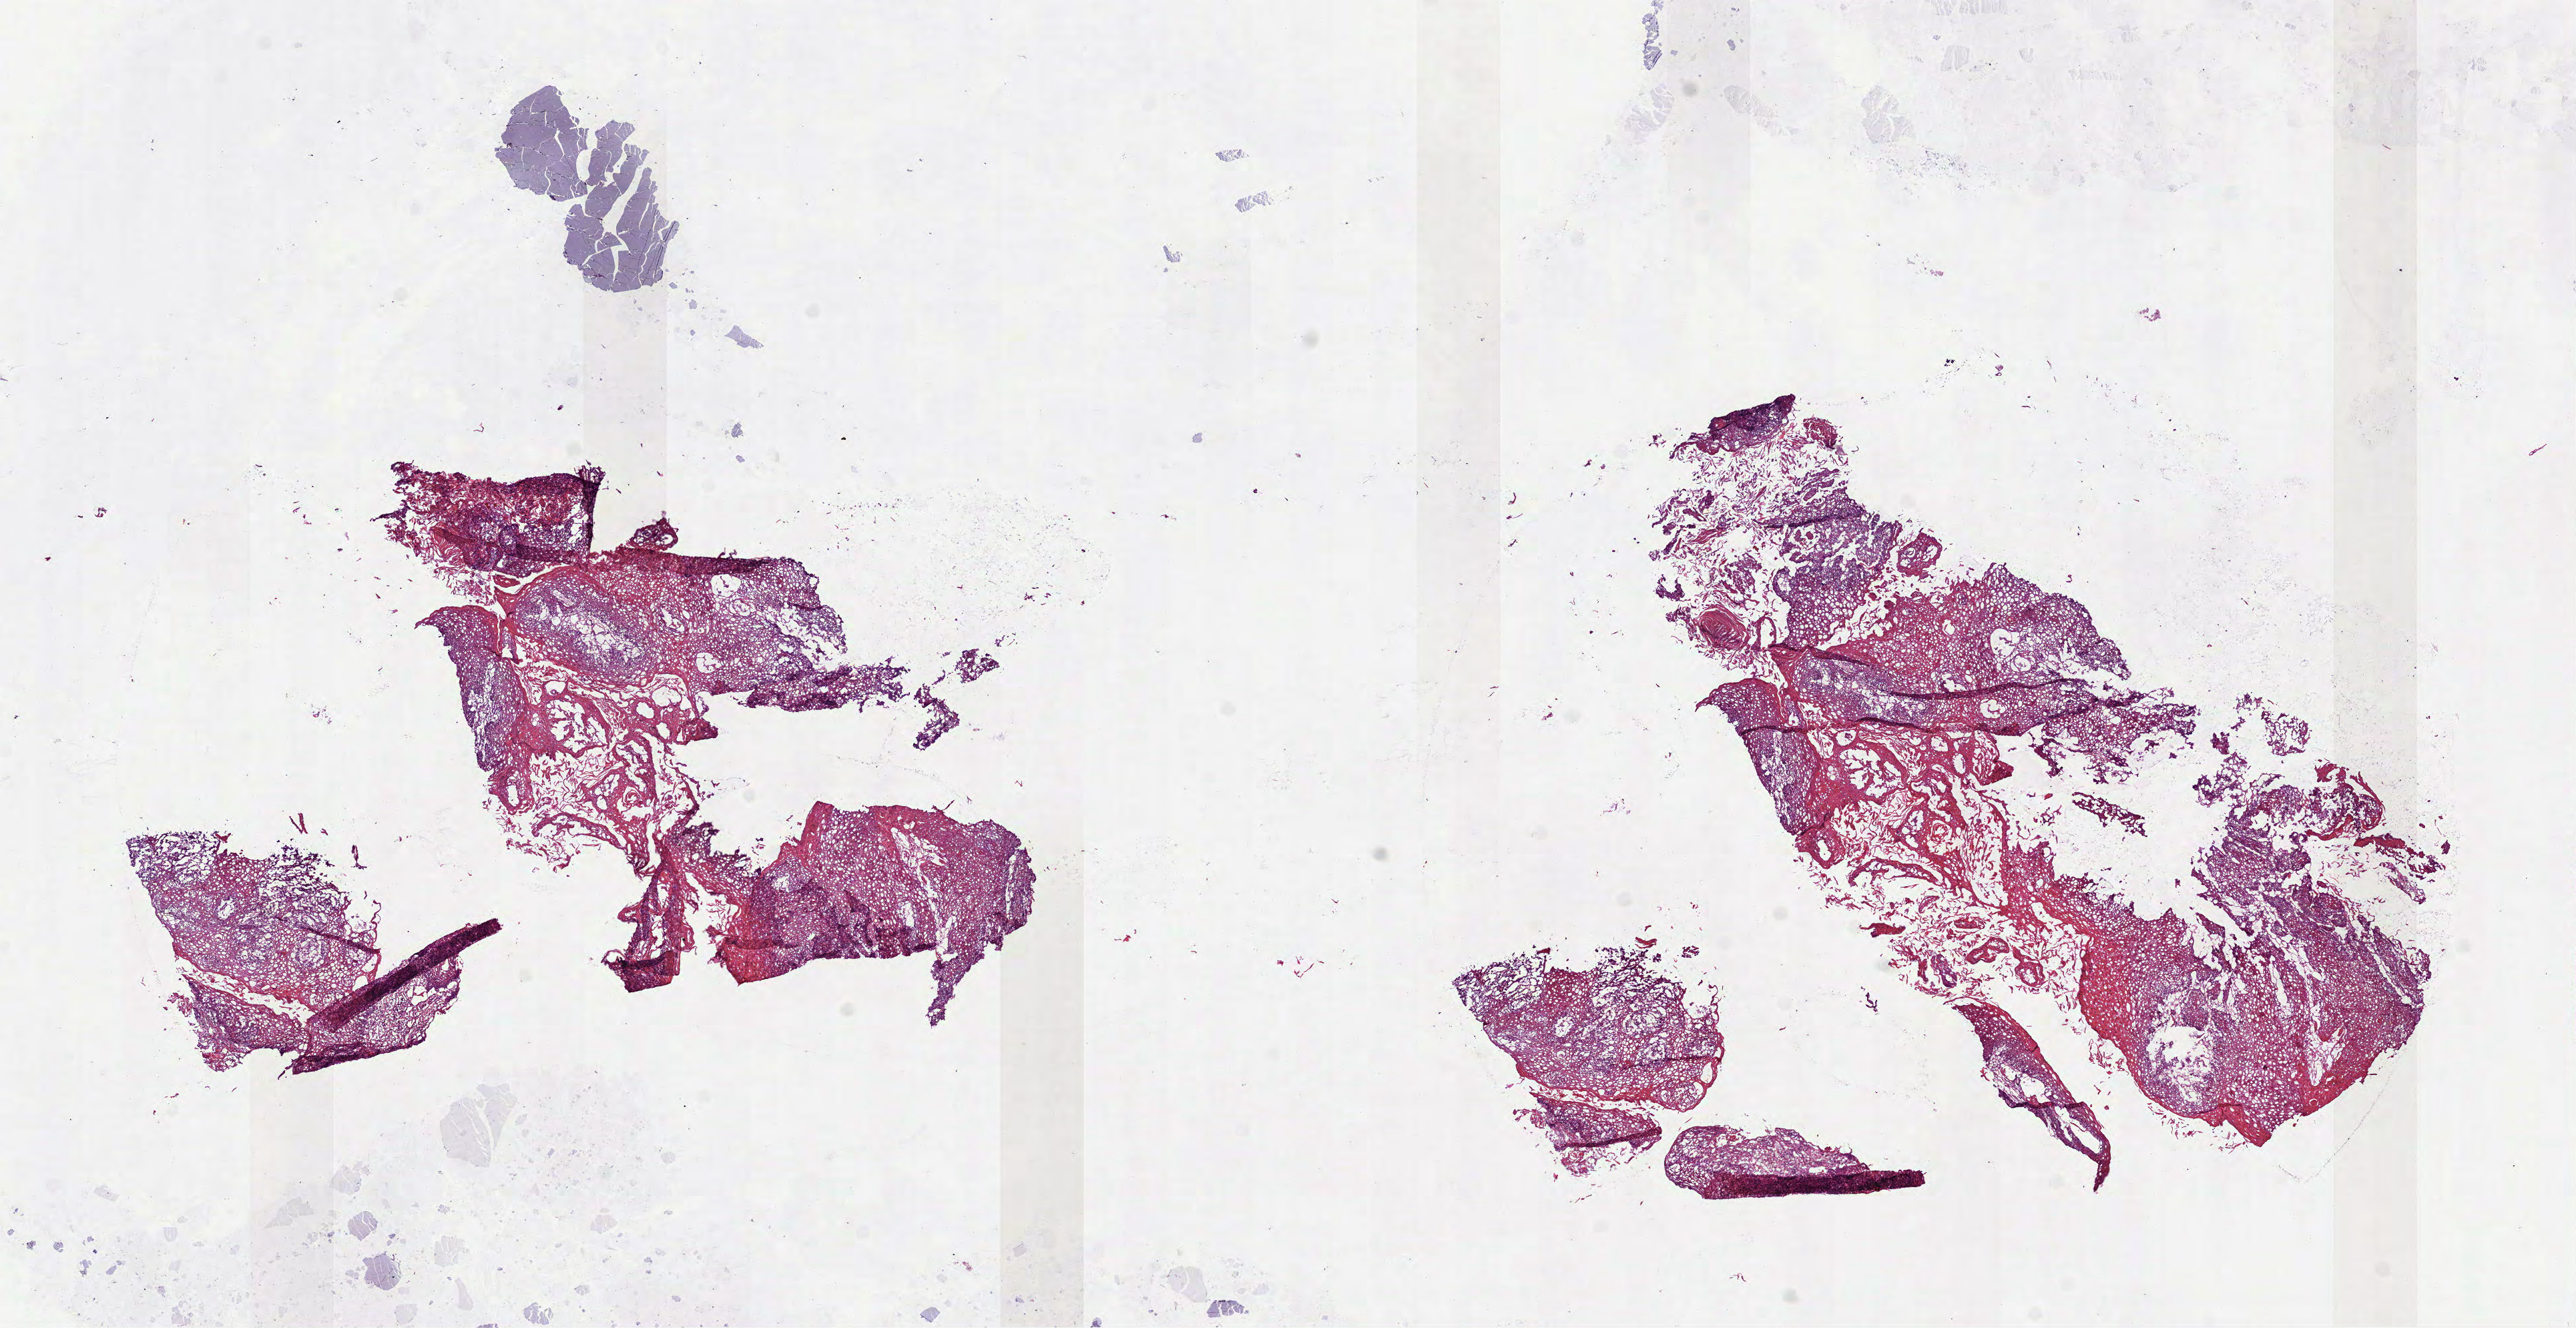
Whole-slide histology image, H&E, shown as a low-resolution overview of the whole scanned area (about 15.6 x 8.0 mm, from a 40x scan). Frozen section from the top of the tissue portion. Head and neck, primary tumour sample. Male, age 62 years at initial diagnosis. Histologic grade: G1 (well differentiated). Slide review estimates, as recorded: tumour cells 95%, tumour nuclei 90%, normal cells 0%, stromal cells 5%, necrosis 0%.
- laterality: left
- AJCC pathologic stage: IVA (7th edition)
- diagnosis: Squamous cell carcinoma, NOS (tongue, NOS)